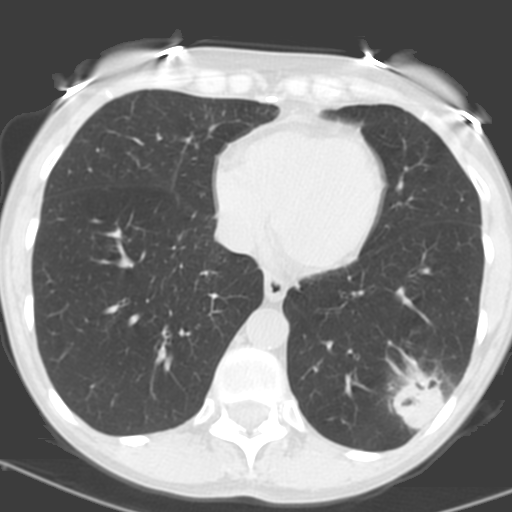
Chest CT (low-dose screening protocol), one axial image. Baseline screening round. Lung window (W 1500 / L -600 HU). 3.2 mm slice thickness. Female participant, aged 56 years at enrolment. Current smoker at enrolment.
Expert-annotated lung lesion, box from (x=379, y=362) to (x=458, y=433) px. Reader record for this screening exam (exam-level; its link to the box is not recorded): non-calcified nodule or mass ≥4 mm, left lower lobe, 31 × 23 mm, poorly defined margins, soft tissue attenuation, pre-existing on the prior screen: no.